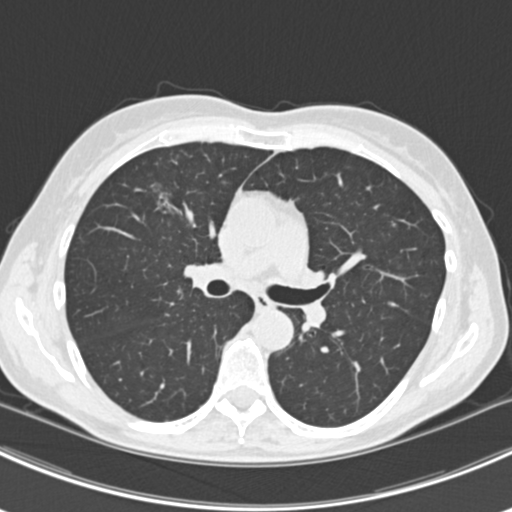
Chest CT (low-dose screening protocol), one axial image; first (baseline) screen; lung window (W 1500 / L -600 HU); 120 kVp; 512 × 512 image matrix, field of view 310 × 310 mm. Female, age 63 years at enrolment. Current smoker at enrolment.
Expert-annotated lung lesion, box from (x=145, y=179) to (x=201, y=234) px. The screening reader recorded 10 non-calcified nodules or masses ≥4 mm on this exam (right lower lobe, right lower lobe, left lower lobe, left lower lobe, right middle lobe, right lower lobe, left lower lobe, left upper lobe, right upper lobe, left upper lobe); which of them this box marks is not recorded. Later outcome: lung cancer diagnosed 751 days after this screen (after the third annual screen) — bronchiolo-alveolar adenocarcinoma, NOS, right upper lobe, right middle lobe, right lower lobe, left upper lobe, left lower lobe, moderately differentiated (G2), stage IV (AJCC 6th edition).